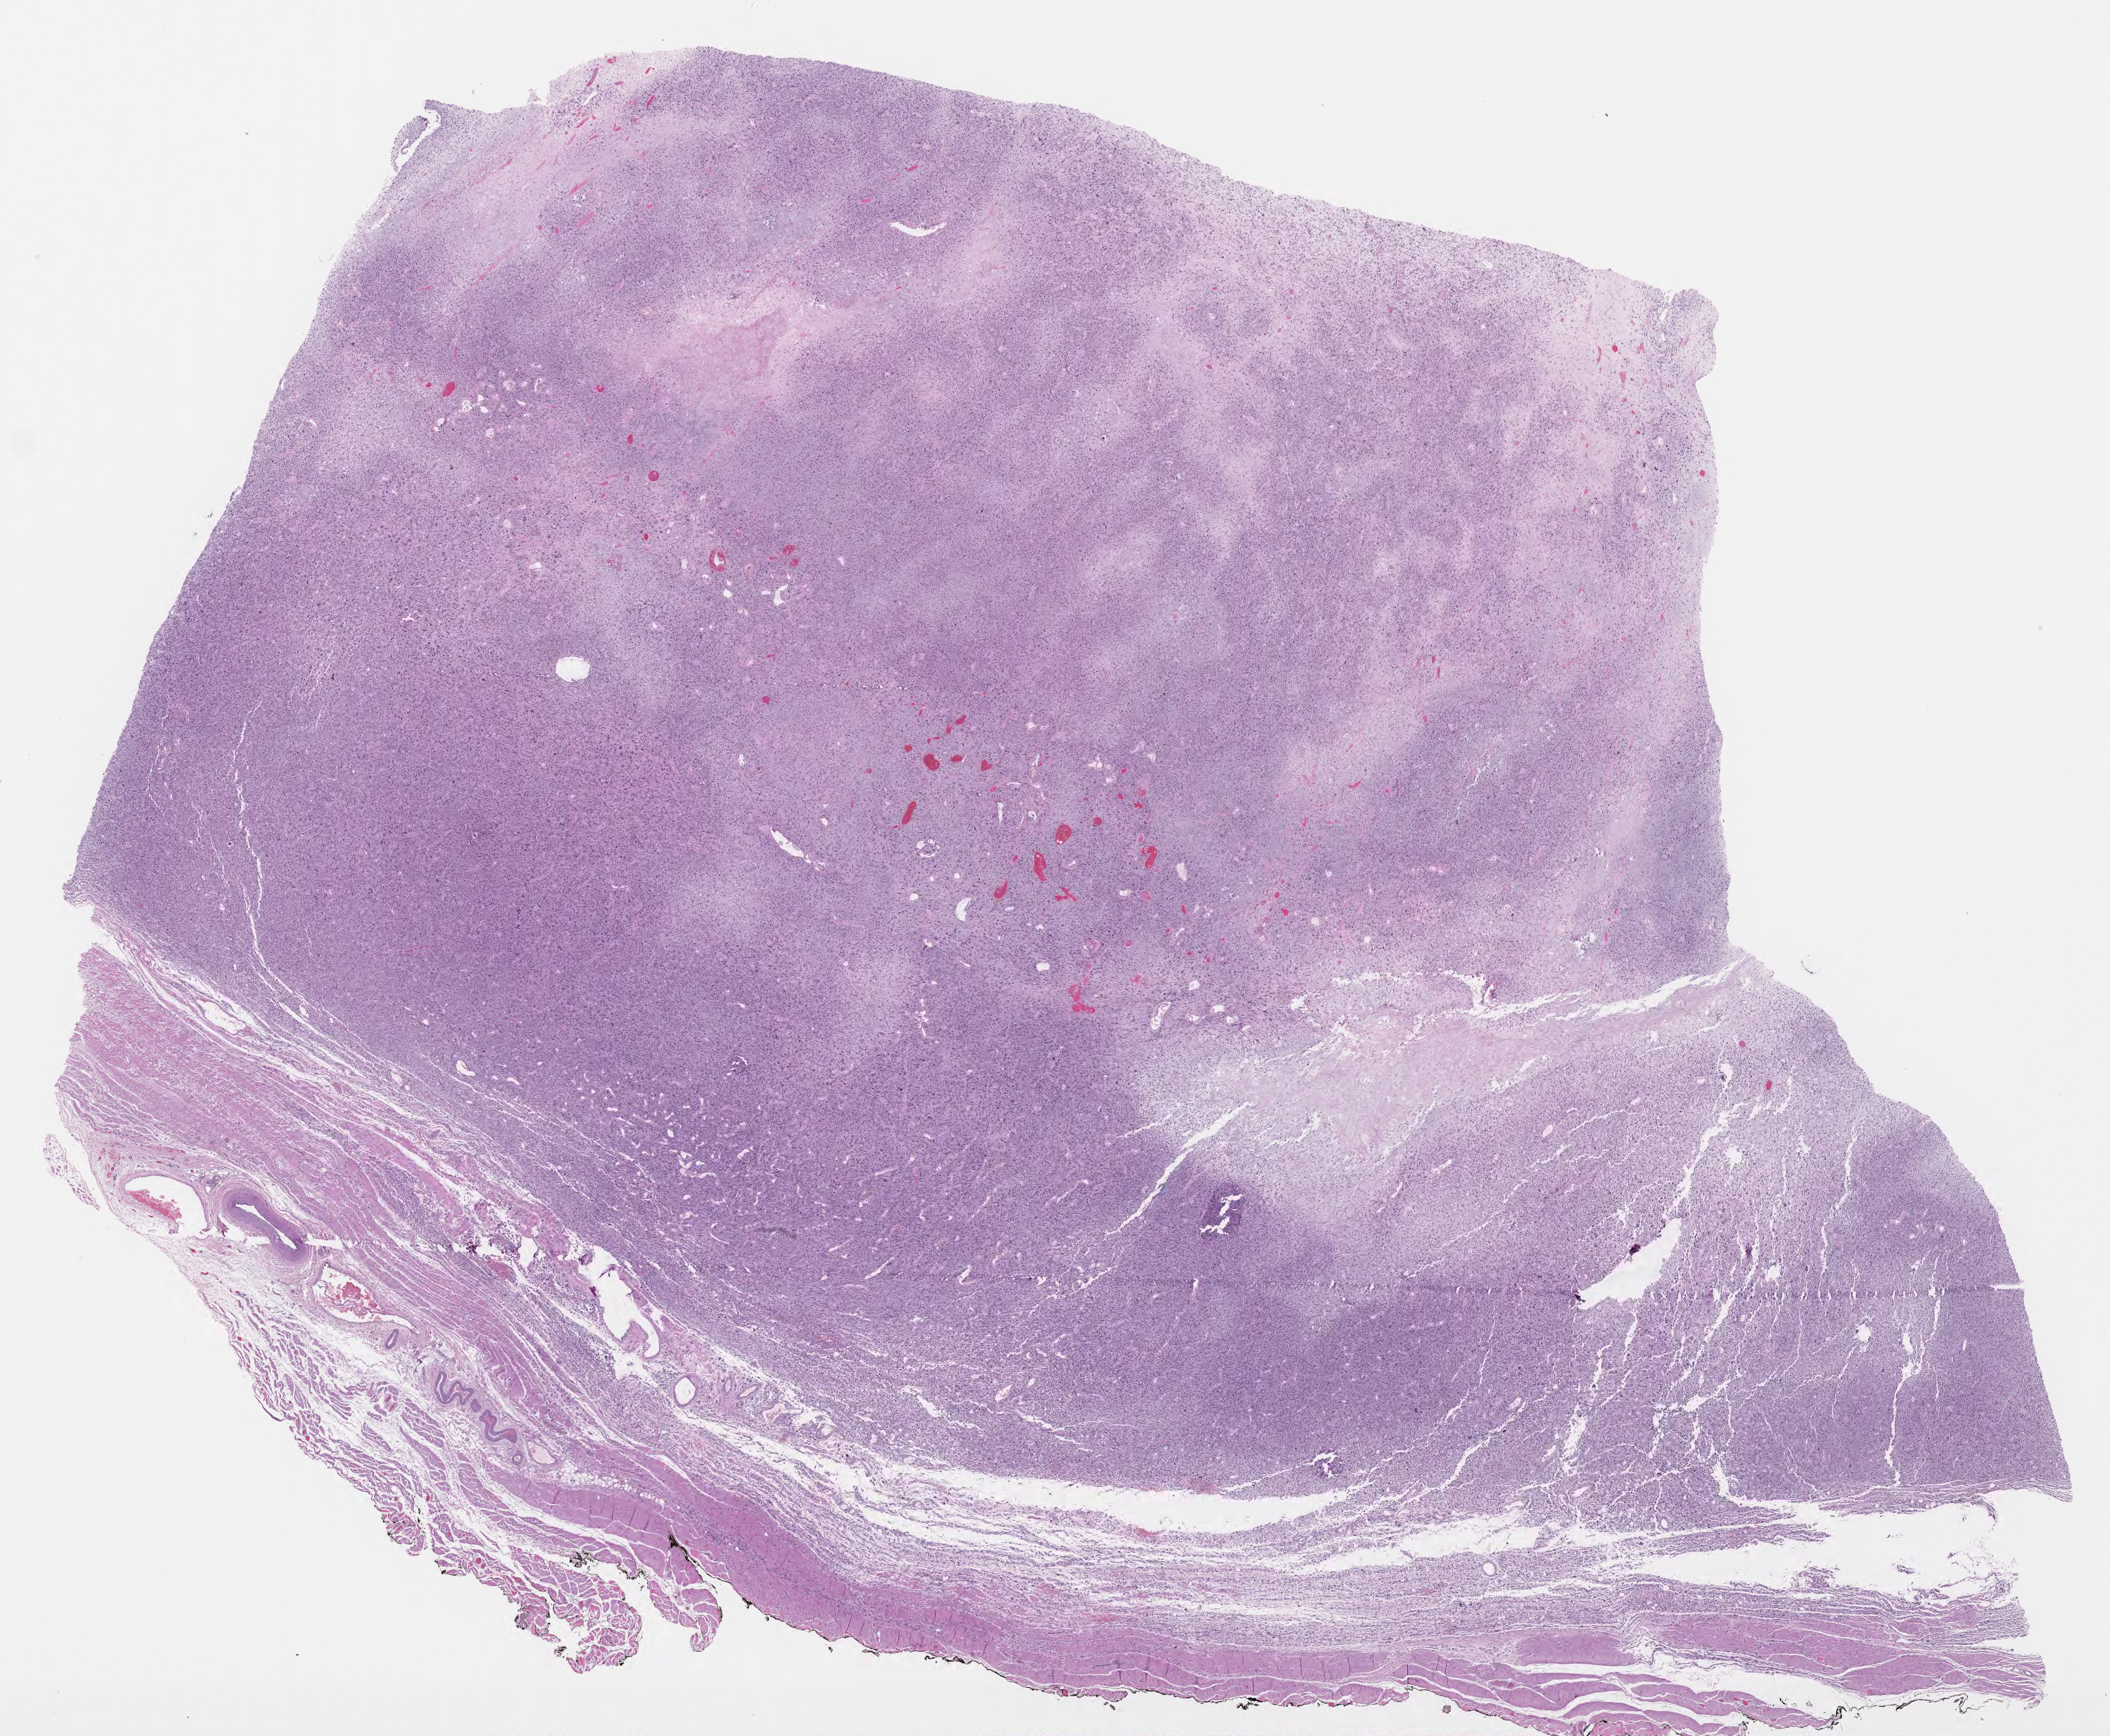
Whole-slide histology image, H&E — whole scanned area (about 26.0 x 21.4 mm, acquisition: 40x scan) shown as a low-resolution overview. Formalin-fixed paraffin-embedded (FFPE) diagnostic section. Primary tumour sample from the connective, subcutaneous and other soft tissues. Female, age 78 years at initial diagnosis.
Histologic diagnosis: Undifferentiated sarcoma (connective, subcutaneous and other soft tissues of lower limb and hip).